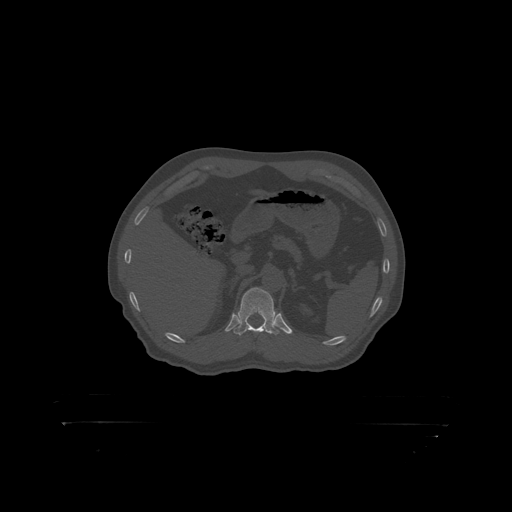
CT including the spine, one axial slice; slice 355 of 399 in the series (ordered by position); reconstruction kernel STANDARD; bone window (W 1800 / L 400 HU); 1.25 mm slice thickness; 512 × 512 image matrix, field of view 650 × 650 mm. Male patient, age 46 years. From the clinical record (not read from this slice): primary cancer: skin.
Outlined on this slice (semi-automatic segmentation, software-assisted and operator-edited):
- T12 vertebra: bounding box <234,288,280,319> (left, top, right, bottom; pixels)